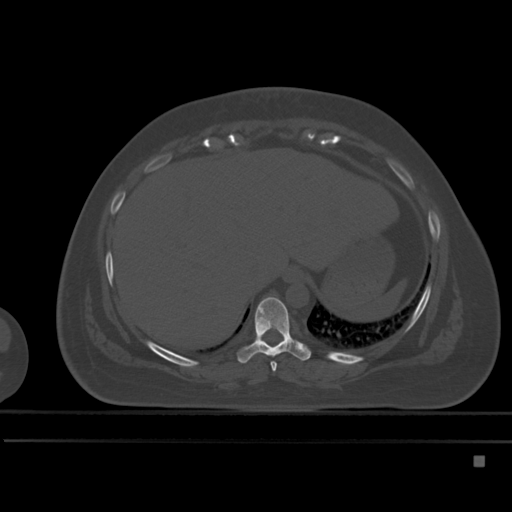
CT including the spine, one axial slice. Position 263 of 495 along the scan axis. Bone window (W 1800 / L 400 HU). 512 × 512 image matrix. Female patient, age 33 years. Case-level facts recorded for this patient, not image findings: primary cancer: breast.
Outlined on this slice (semi-automatically segmented with operator editing):
- T8 vertebra: bounding box <271,361,277,371> (left, top, right, bottom; pixels)
- T9 vertebra: <237,297,311,364>